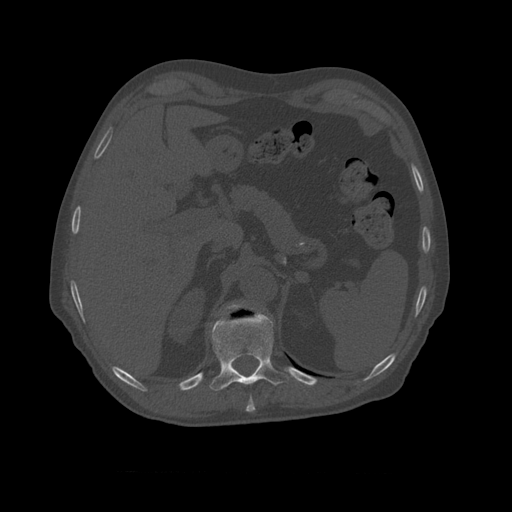
CT including the spine, one axial slice; position 401 of 450 along the scan axis; 120 kVp; bone window (W 1800 / L 400 HU); 512 × 512 image matrix, field of view 405 × 405 mm. Patient age 75 years. Case-level facts recorded for this patient, not image findings: primary cancer: prostate.
Outlined on this slice (semi-automatically segmented with operator editing):
- T10 vertebra: bounding box (x1, y1, x2, y2) in pixels: (209, 308, 289, 392)
- T11 vertebra: (221, 301, 261, 321)
- T9 vertebra: (247, 396, 256, 410)